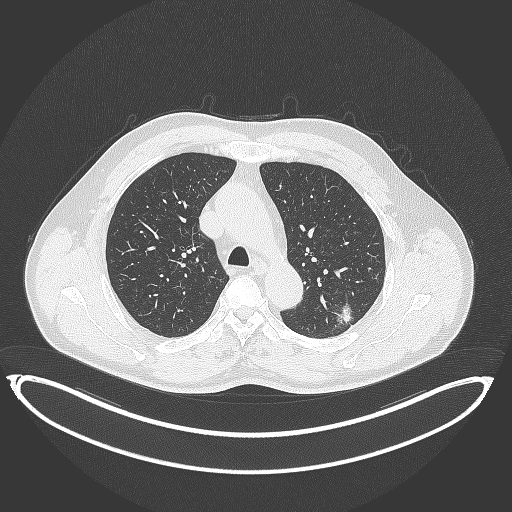
Chest CT, one axial slice; position 256 of 399 along the scan axis; reconstruction kernel B70f; lung window (W 1500 / L -600 HU); 1 mm slice thickness; 512 × 512 image matrix. Male patient, age 58 years. From the clinical record (not read from this slice): clinical TNM (as recorded): T1c N0 M0; histopathological grade: G1-2.
Outlined on this slice (rectangle marked by the reading radiologist):
- lung tumour (recorded histology: adenocarcinoma): bounding box <330,297,358,325> (left, top, right, bottom; pixels)